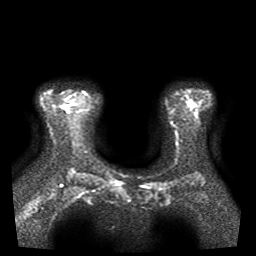
Breast MRI, one axial slice; position 30 of 41 along the scan axis; diffusion-weighted series; image 2 of 4 stored at this slice position (different b-values; order by instance number); 1.5 T; 256 × 256 image matrix. Female patient.
Annotated regions visible in this slice (expert manual segmentation):
- tumour on diffusion-weighted imaging: bounding box <70,103,77,106> (left, top, right, bottom; pixels)